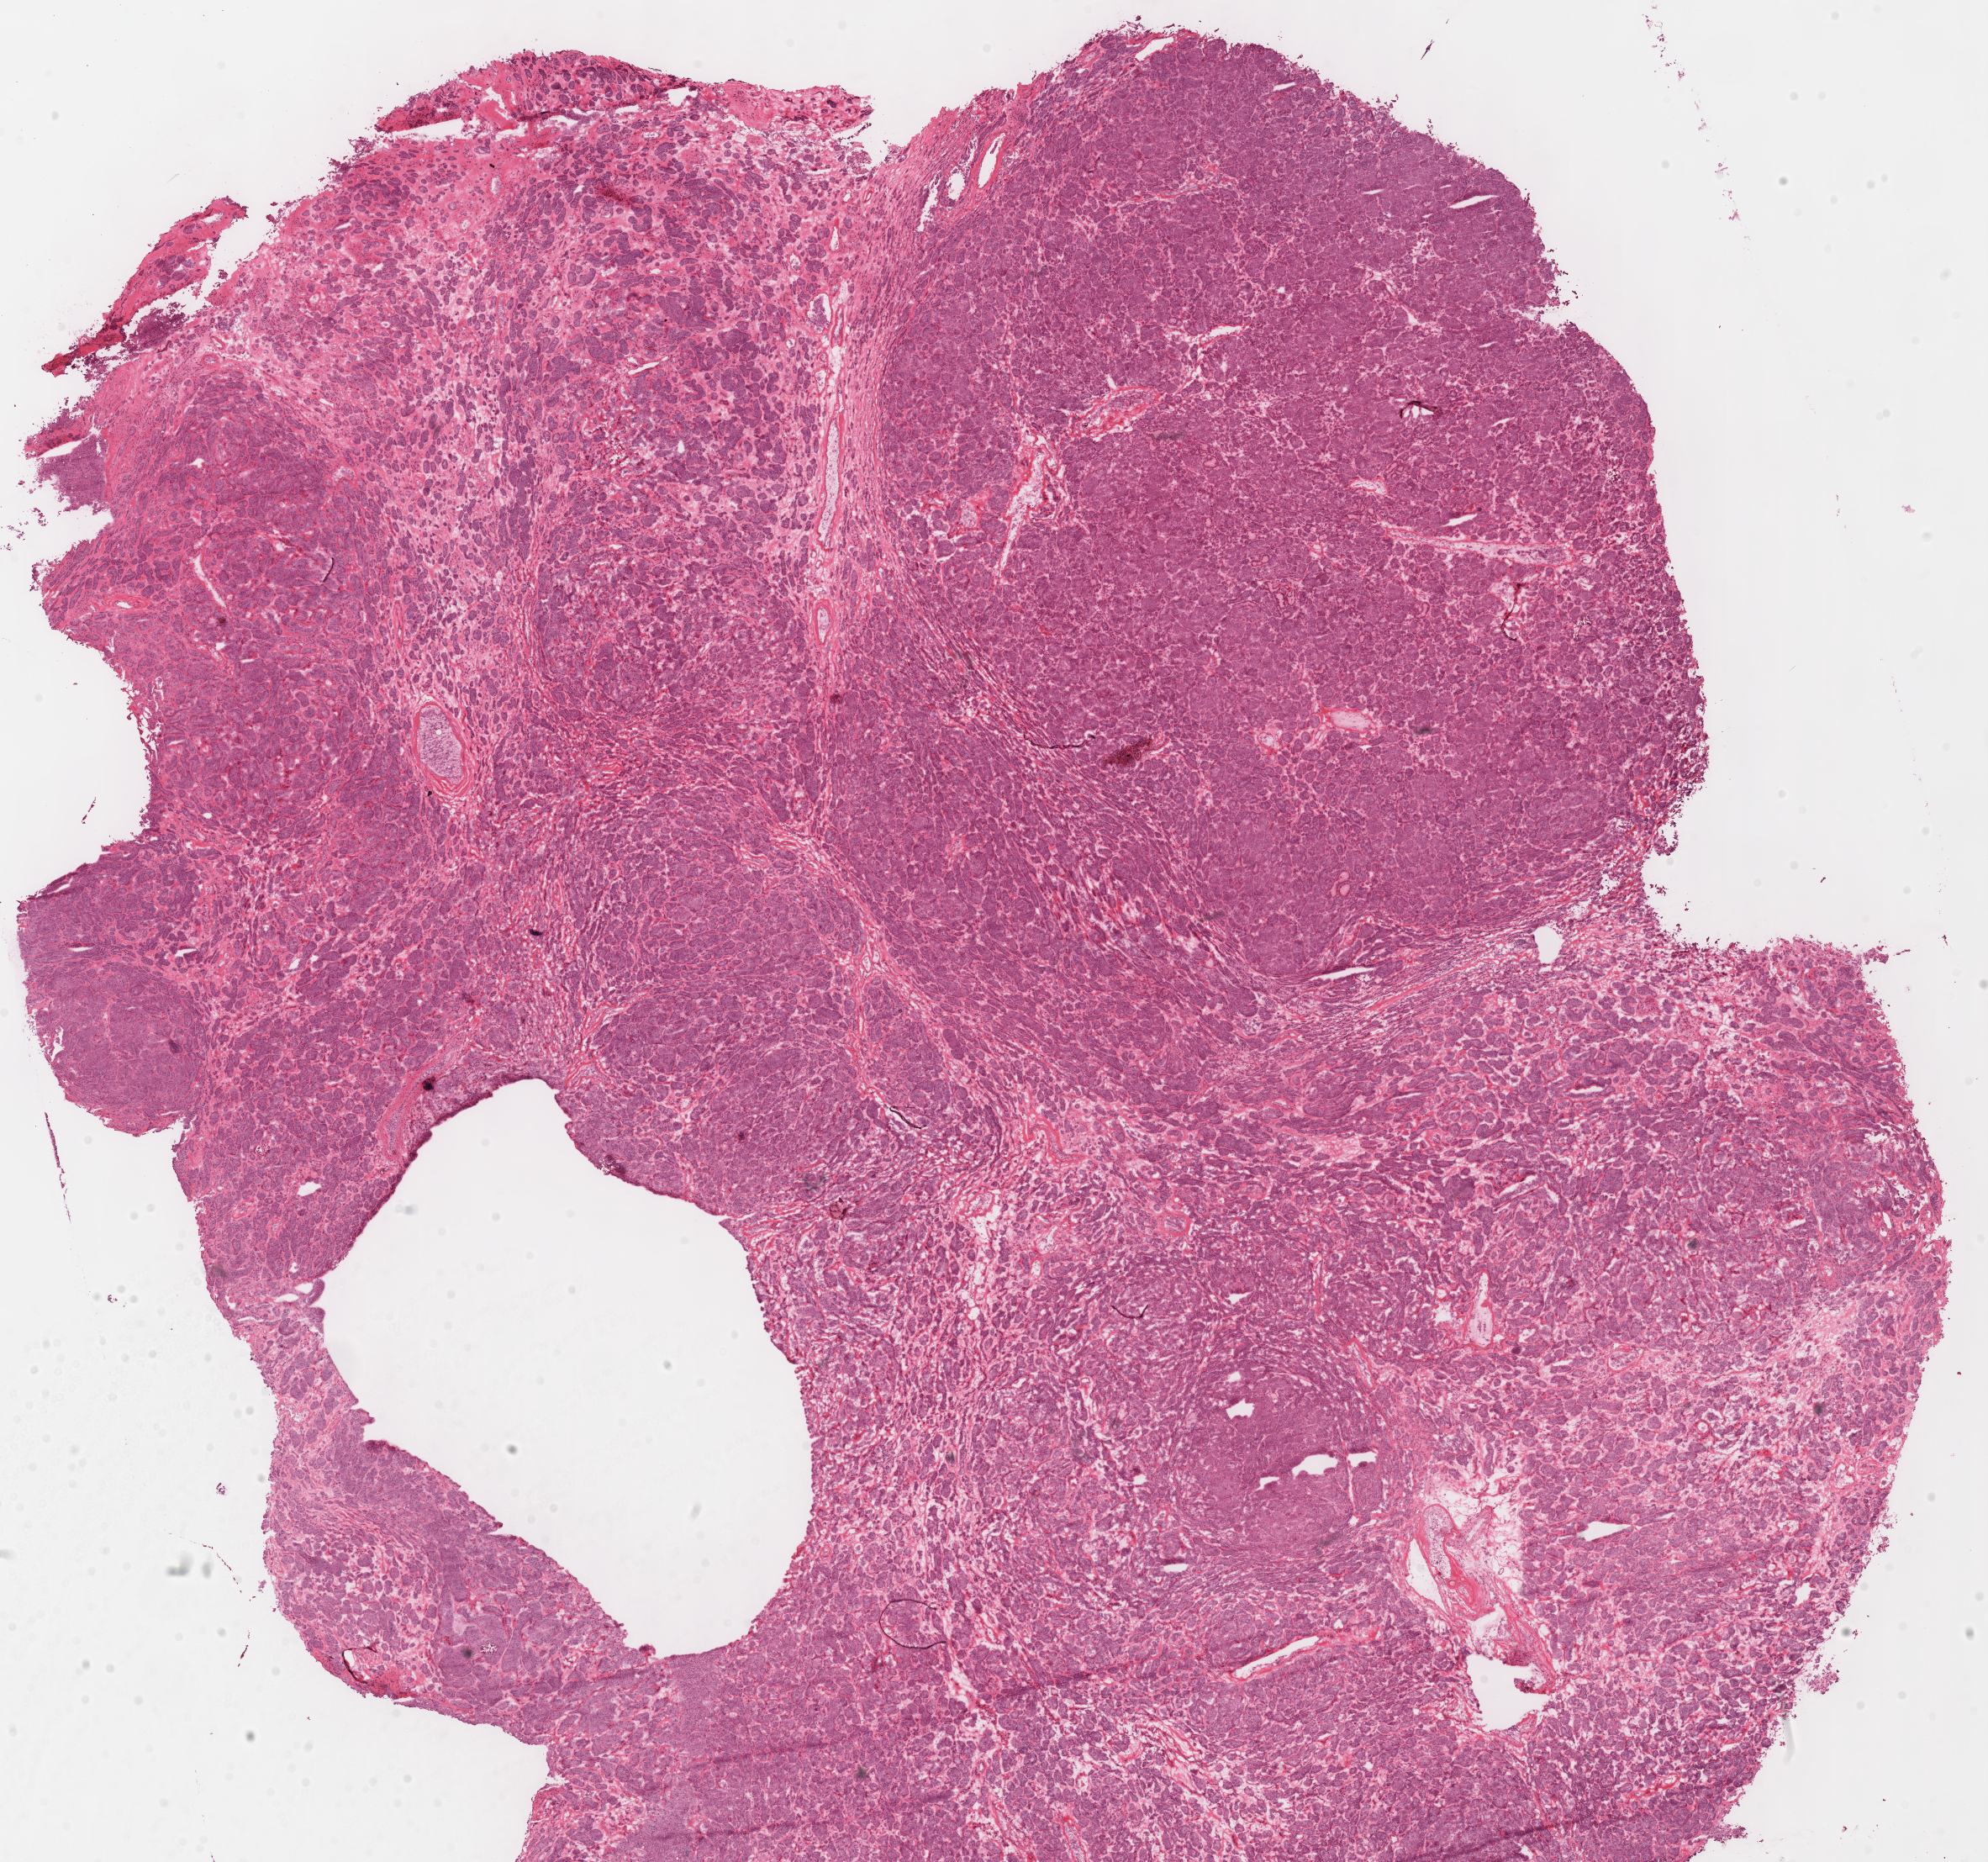
Whole-slide histology image, H&E, a low-resolution overview of the entire scanned area, about 18.6 x 17.4 mm, frozen section from the top of the tissue portion, kidney, primary tumour sample. Male patient; age at initial diagnosis 51 years. Slide review estimates, as recorded: tumour cells 85%, tumour nuclei 90%, normal cells 0%, stromal cells 15%, necrosis 0%.
Laterality: right. TNM: T3a N0 M0. Histologic diagnosis: Renal cell carcinoma, chromophobe type. Lymph nodes positive (case pathology): 0 of 15 examined. AJCC pathologic stage: III (6th edition).